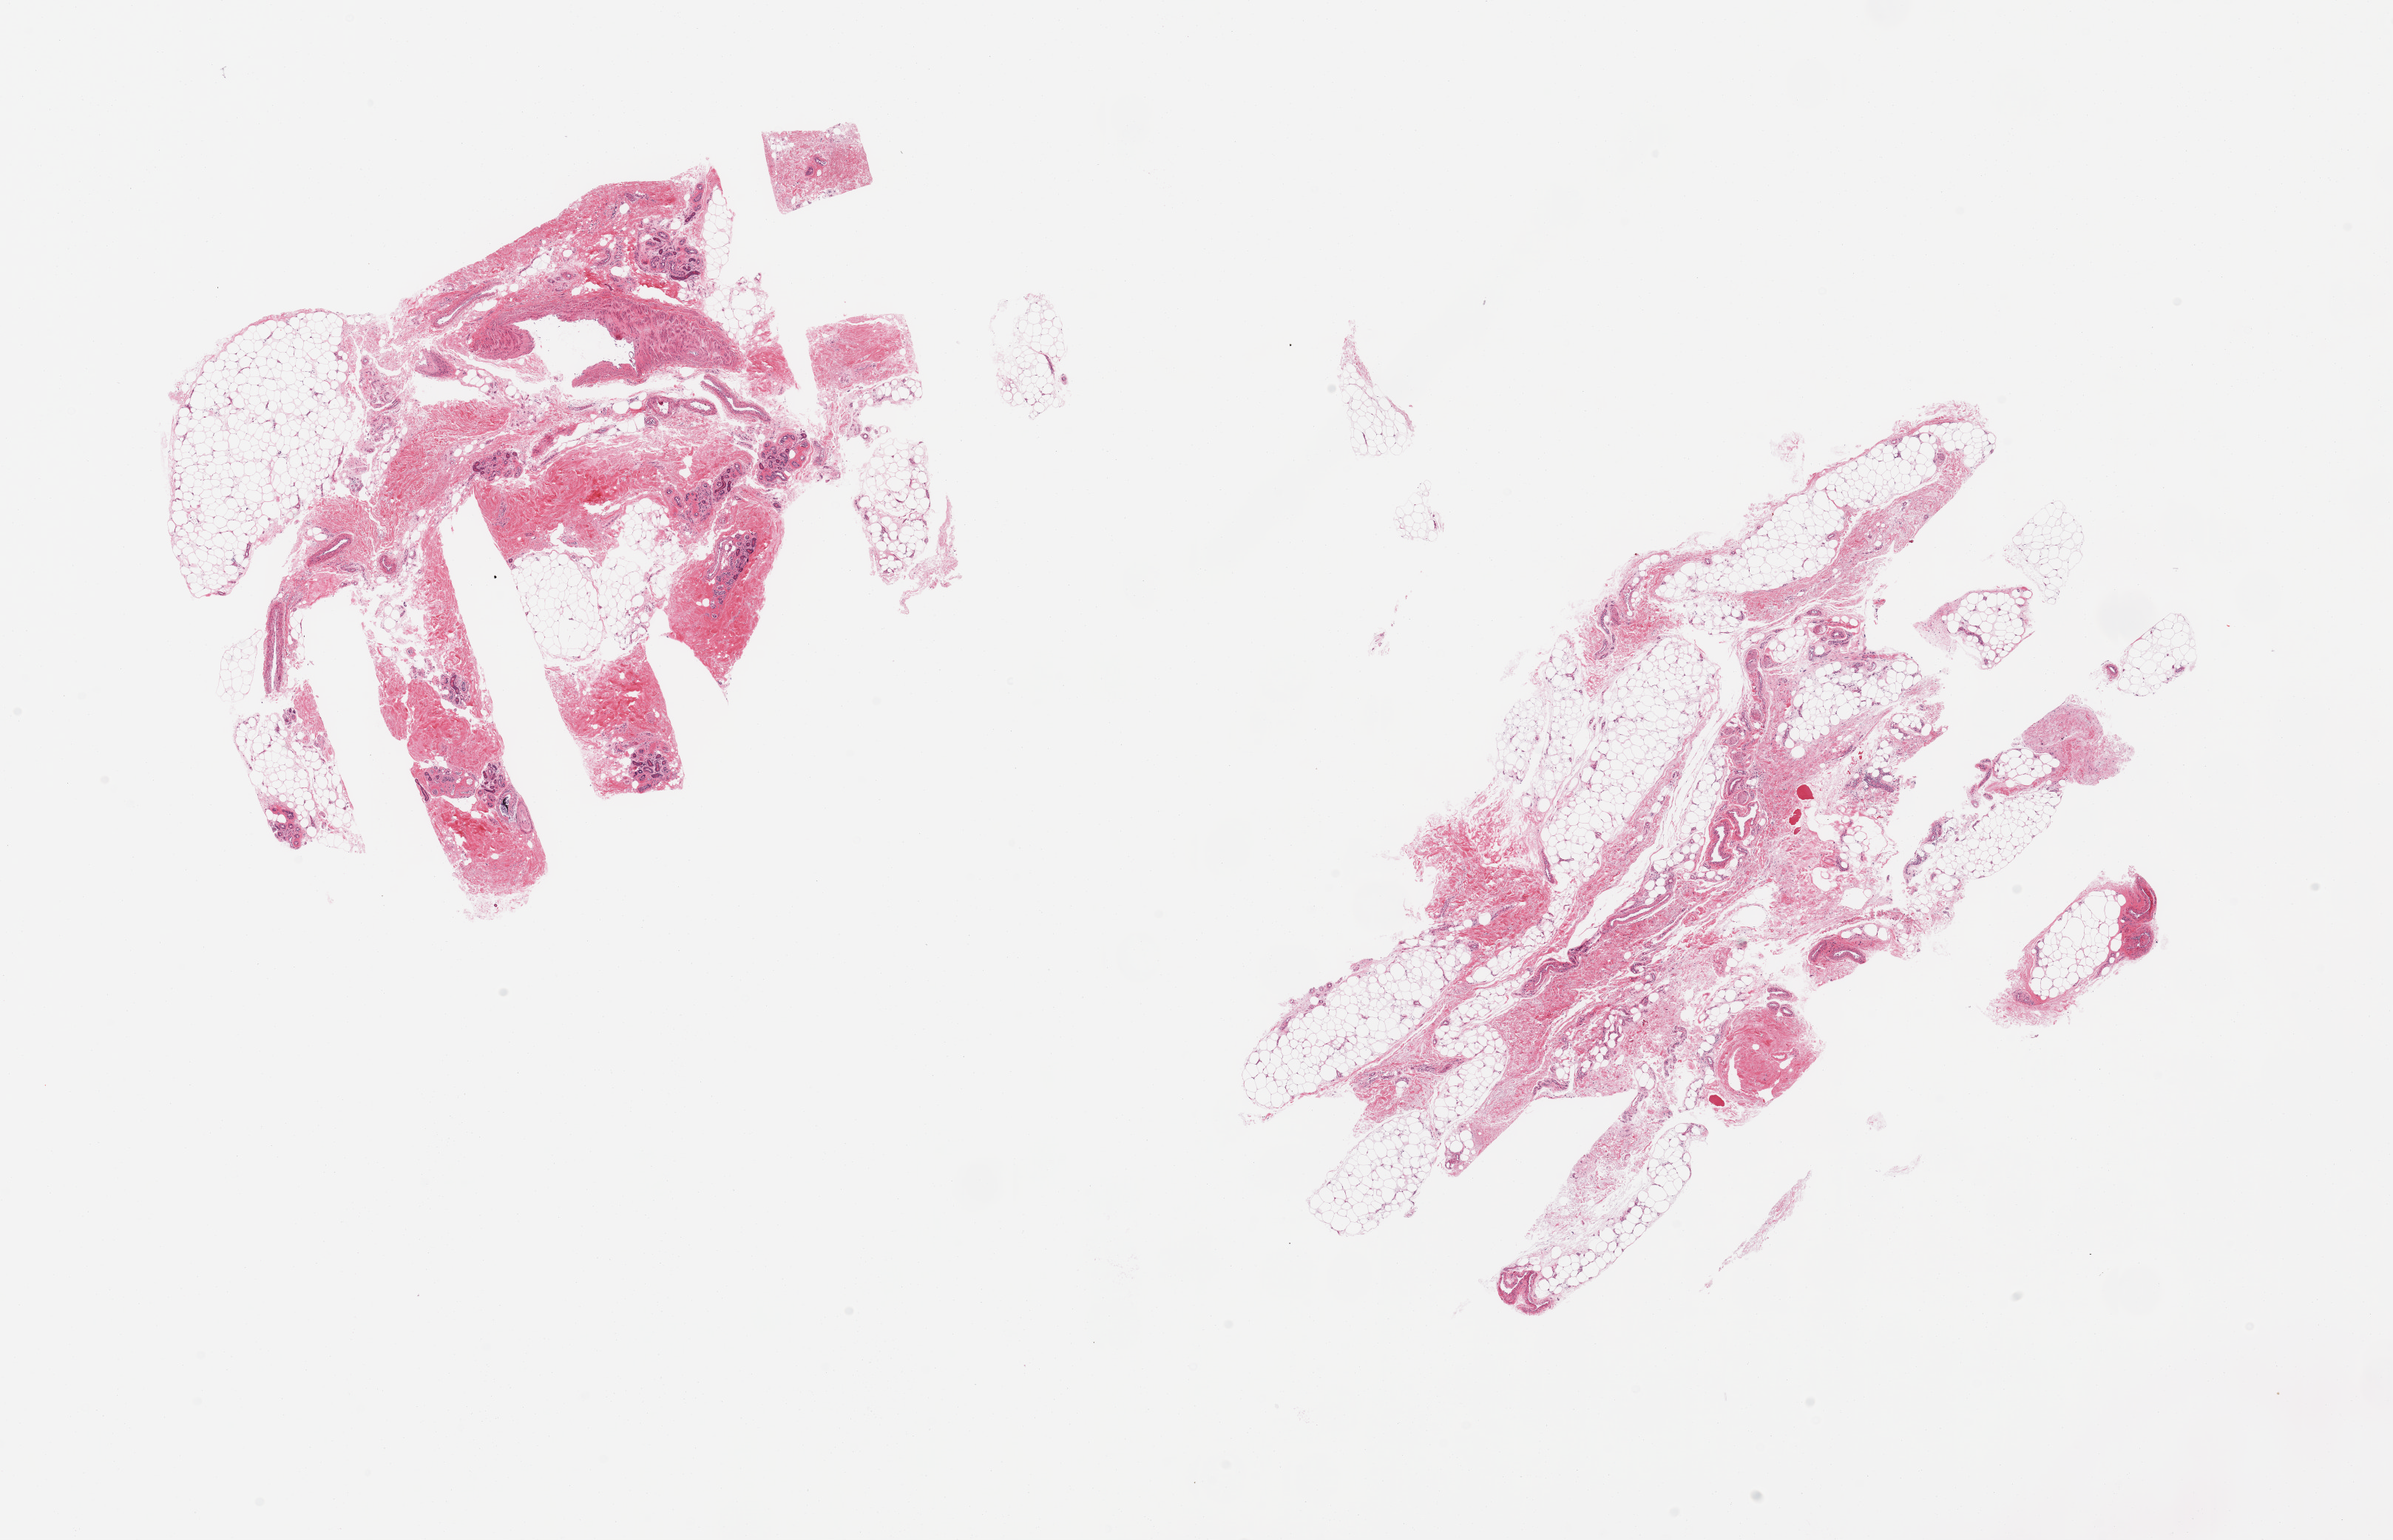
Digitized haematoxylin and eosin-stained section, brightfield, whole scanned area (about 25.6 x 16.5 mm, from a 20x scan) shown as a low-resolution overview; PAXgene-fixed paraffin-embedded (PFPE) section; sampled site (target tissue): adipose tissue; donor tissue sample. Male donor.
* reviewer comment on this tissue sample: 2 pieces; 1 piece has 70% fat, 30% fibrous content; other piece has 40% fat, 60% fibrous dermis with sweat glands